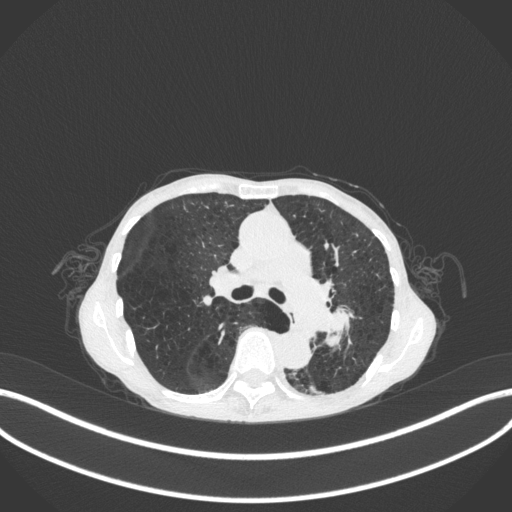
Chest CT, one axial slice. Position 174 of 347 along the scan axis. Lung window (W 1500 / L -600 HU). 512 × 512 image matrix, field of view 400 × 400 mm. Female patient, age 70 years. Case-level facts recorded for this patient, not image findings: clinical TNM (as recorded): T3 N0 M0; histopathological grade: G3.
Structures marked on this image (rectangle marked by the reading radiologist):
- lung tumour (recorded histology: small cell carcinoma): box from (x=317, y=301) to (x=365, y=355) px